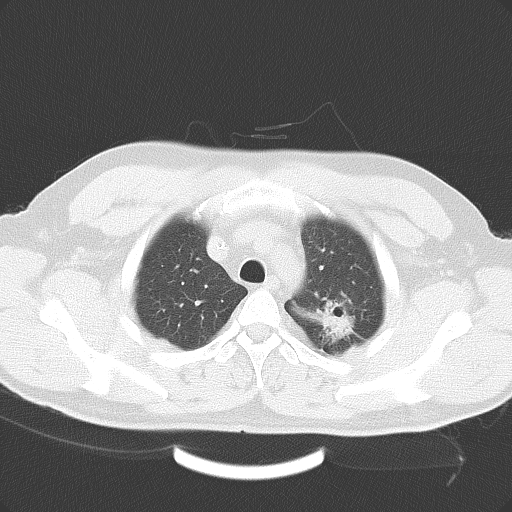
Chest CT, one axial slice. Position 32 of 41 along the scan axis. Reconstruction kernel B70f. 120 kVp. Lung window (W 1500 / L -600 HU). 5 mm slice thickness. 512 × 512 image matrix. Male patient, age 45 years. Case-level facts recorded for this patient, not image findings: clinical TNM (as recorded): T2 N0 M0.
Annotated regions visible in this slice (bounding box drawn by a radiologist):
- lung tumour (recorded histology: adenocarcinoma): box from (x=289, y=295) to (x=369, y=351) px